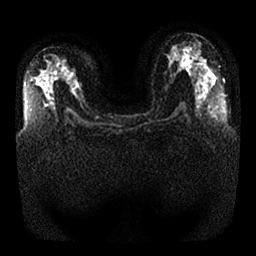
Breast MRI, one axial slice; slice 14 of 32 in the series (ordered by position); diffusion-weighted series; image 2 of 4 stored at this slice position (different b-values; order by instance number); 1.5 T; 256 × 256 image matrix, field of view 350 × 350 mm. Female patient.
Outlined on this slice (manually delineated by an expert):
- tumour on diffusion-weighted imaging: bounding box <71,84,77,92> (left, top, right, bottom; pixels)